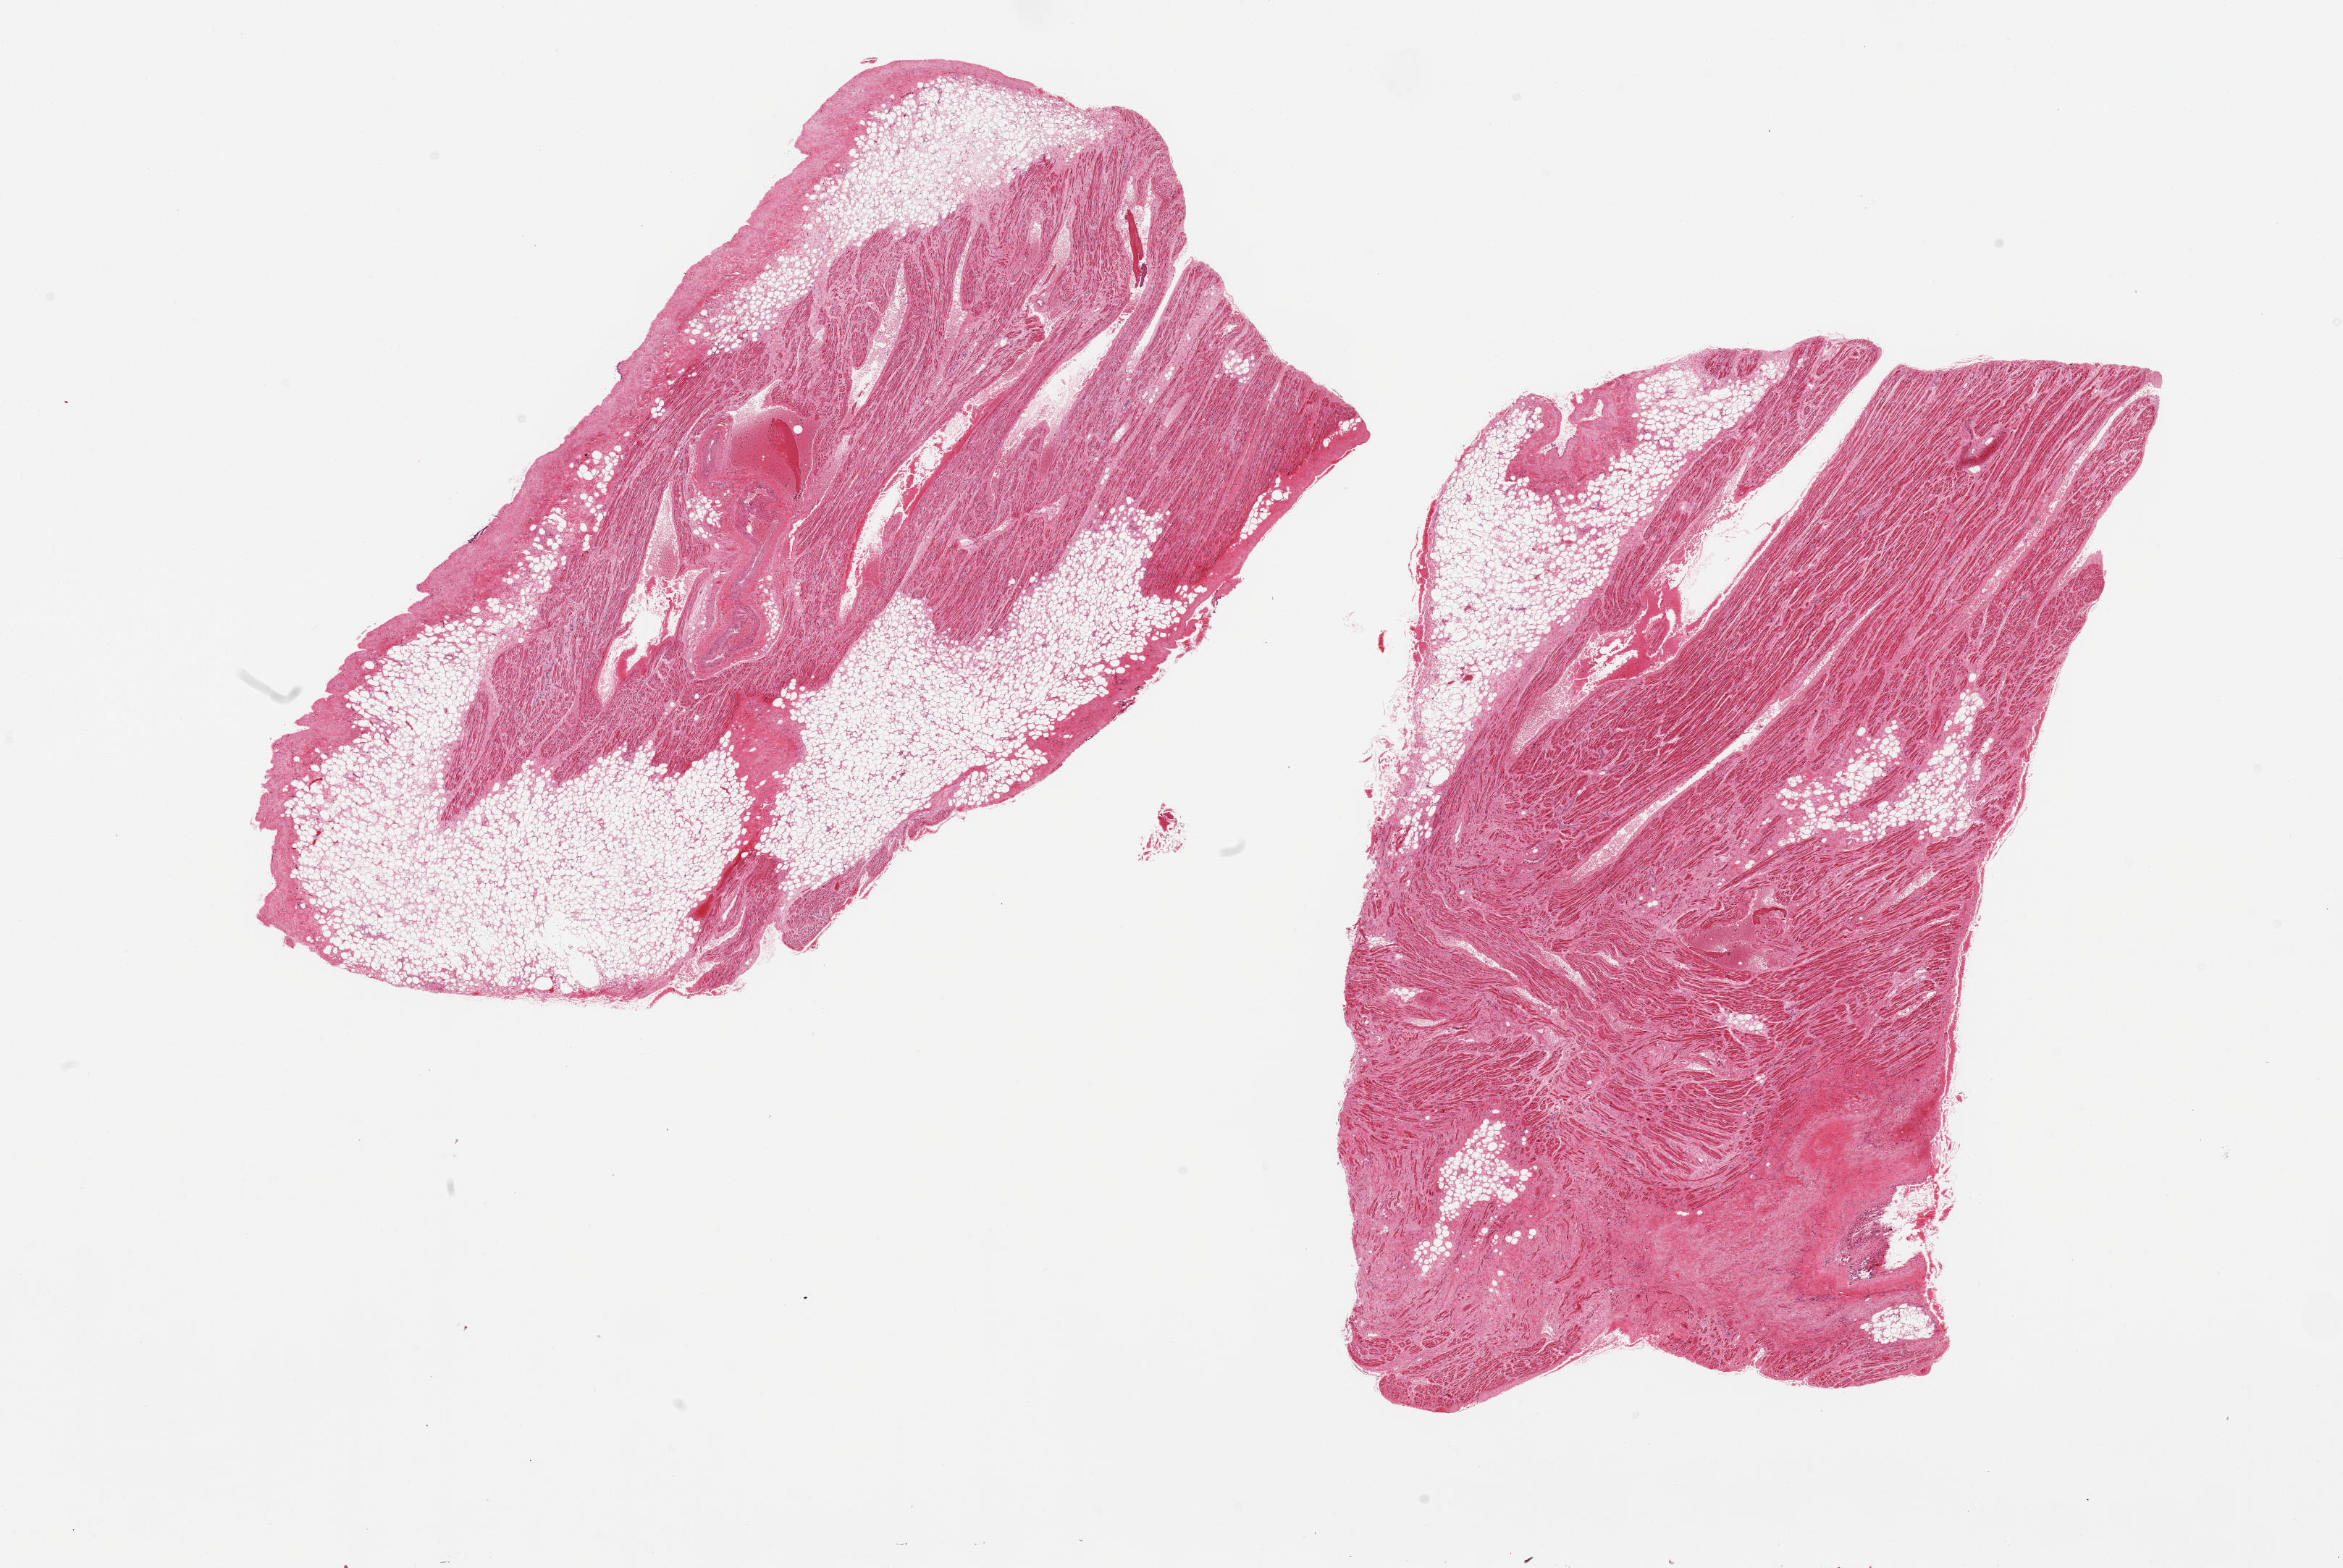
Whole-slide image, hematoxylin and eosin (H&E) stain, brightfield — whole scanned area (about 25.6 x 17.1 mm) shown as a low-resolution overview, PAXgene-fixed, paraffin-embedded tissue, section of auricular appendage (target tissue), donor tissue sample. Donor: male.
- review note (as recorded): 2 pieces; external & internal fat occupies 50% & 25%